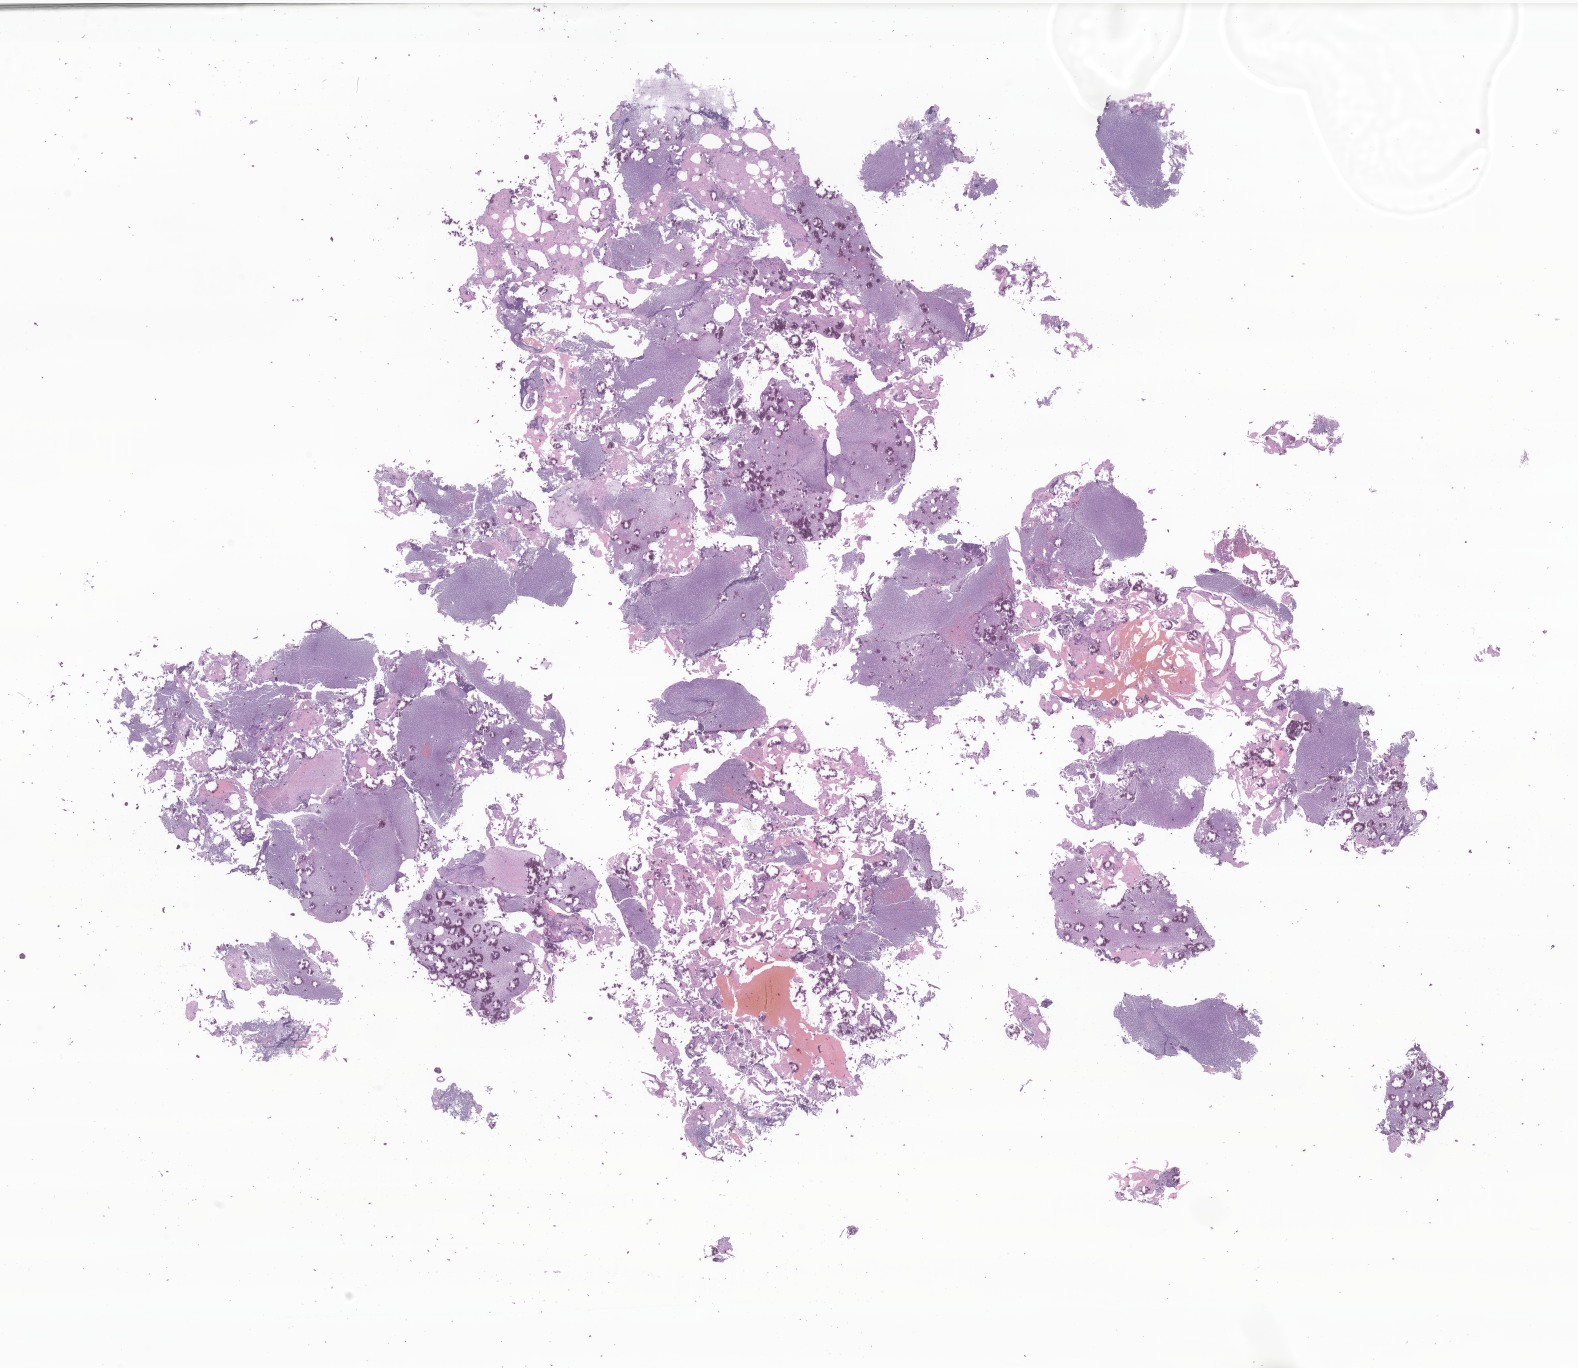
Digitized haematoxylin and eosin-stained section of tumor tissue from the pineal gland — whole scanned area (about 26.6 x 23.1 mm) shown as a low-resolution overview. Formalin-fixed paraffin-embedded section. Female patient, age 191 months.
Recorded diagnosis: Pinealoma.